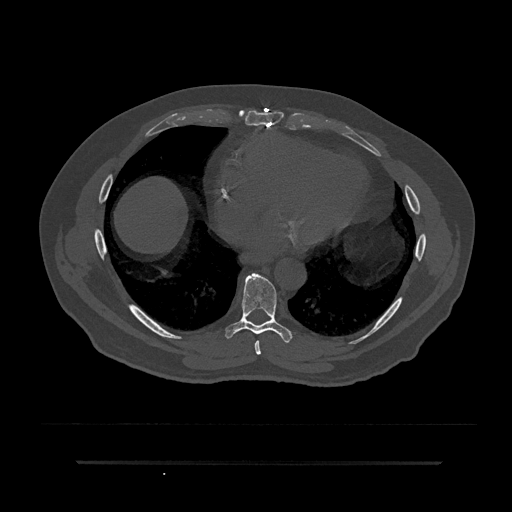
CT including the spine, one axial slice. Position 432 of 797 along the scan axis. Reconstruction kernel Br40s/3. 120 kVp. Bone window (W 1800 / L 400 HU). 512 × 512 image matrix, field of view 464 × 464 mm. Patient: male, 59 years. From the clinical record (not read from this slice): primary cancer: bile ducts; vertebrae with lytic lesions (as recorded): T10.
Structures marked on this image (semi-automatically segmented with operator editing):
- T7 vertebra: bounding box [x1, y1, x2, y2] px = [254, 341, 261, 355]
- T8 vertebra: [225, 273, 292, 343]